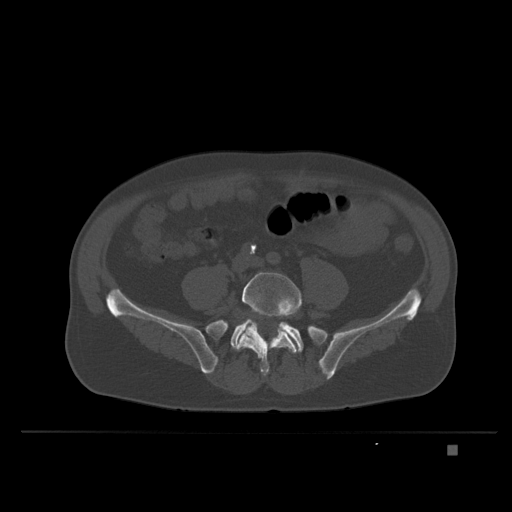
CT including the spine, one axial slice; slice 53 of 435 in the series (ordered by position); bone window (W 1800 / L 400 HU); 1.5 mm slice thickness; 512 × 512 image matrix. Patient: male, 73 years. From the clinical record (not read from this slice): primary cancer: skin.
Annotated regions visible in this slice (semi-automatically segmented with operator editing):
- L5 vertebra: bounding box [x1, y1, x2, y2] px = [237, 272, 302, 376]